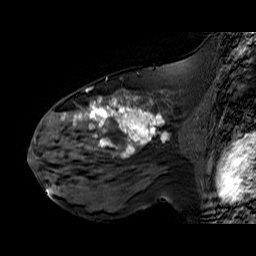
Breast MRI (dynamic contrast-enhanced), one sagittal slice. Dynamic contrast-enhanced series, time point 2 of 6 at this slice position (early post-contrast). 1.5 T. TE 6.3 ms, TR 32.9 ms. 256 × 256 image matrix, field of view 200 × 200 mm. Female patient. Case-level facts recorded for this patient, not image findings: setting: breast cancer imaged before/during neoadjuvant chemotherapy; receptor status: HER2-positive.
Outlined on this slice (semi-automatically segmented with operator editing):
- analysis volume of interest (the breast-tissue region the enhancement analysis was run in; not a lesion): bounding box <48,92,195,174> (left, top, right, bottom; pixels)
- tumour enhancement mask (voxels above the 100 % enhancement threshold inside the analysis volume of interest): <61,96,163,158>